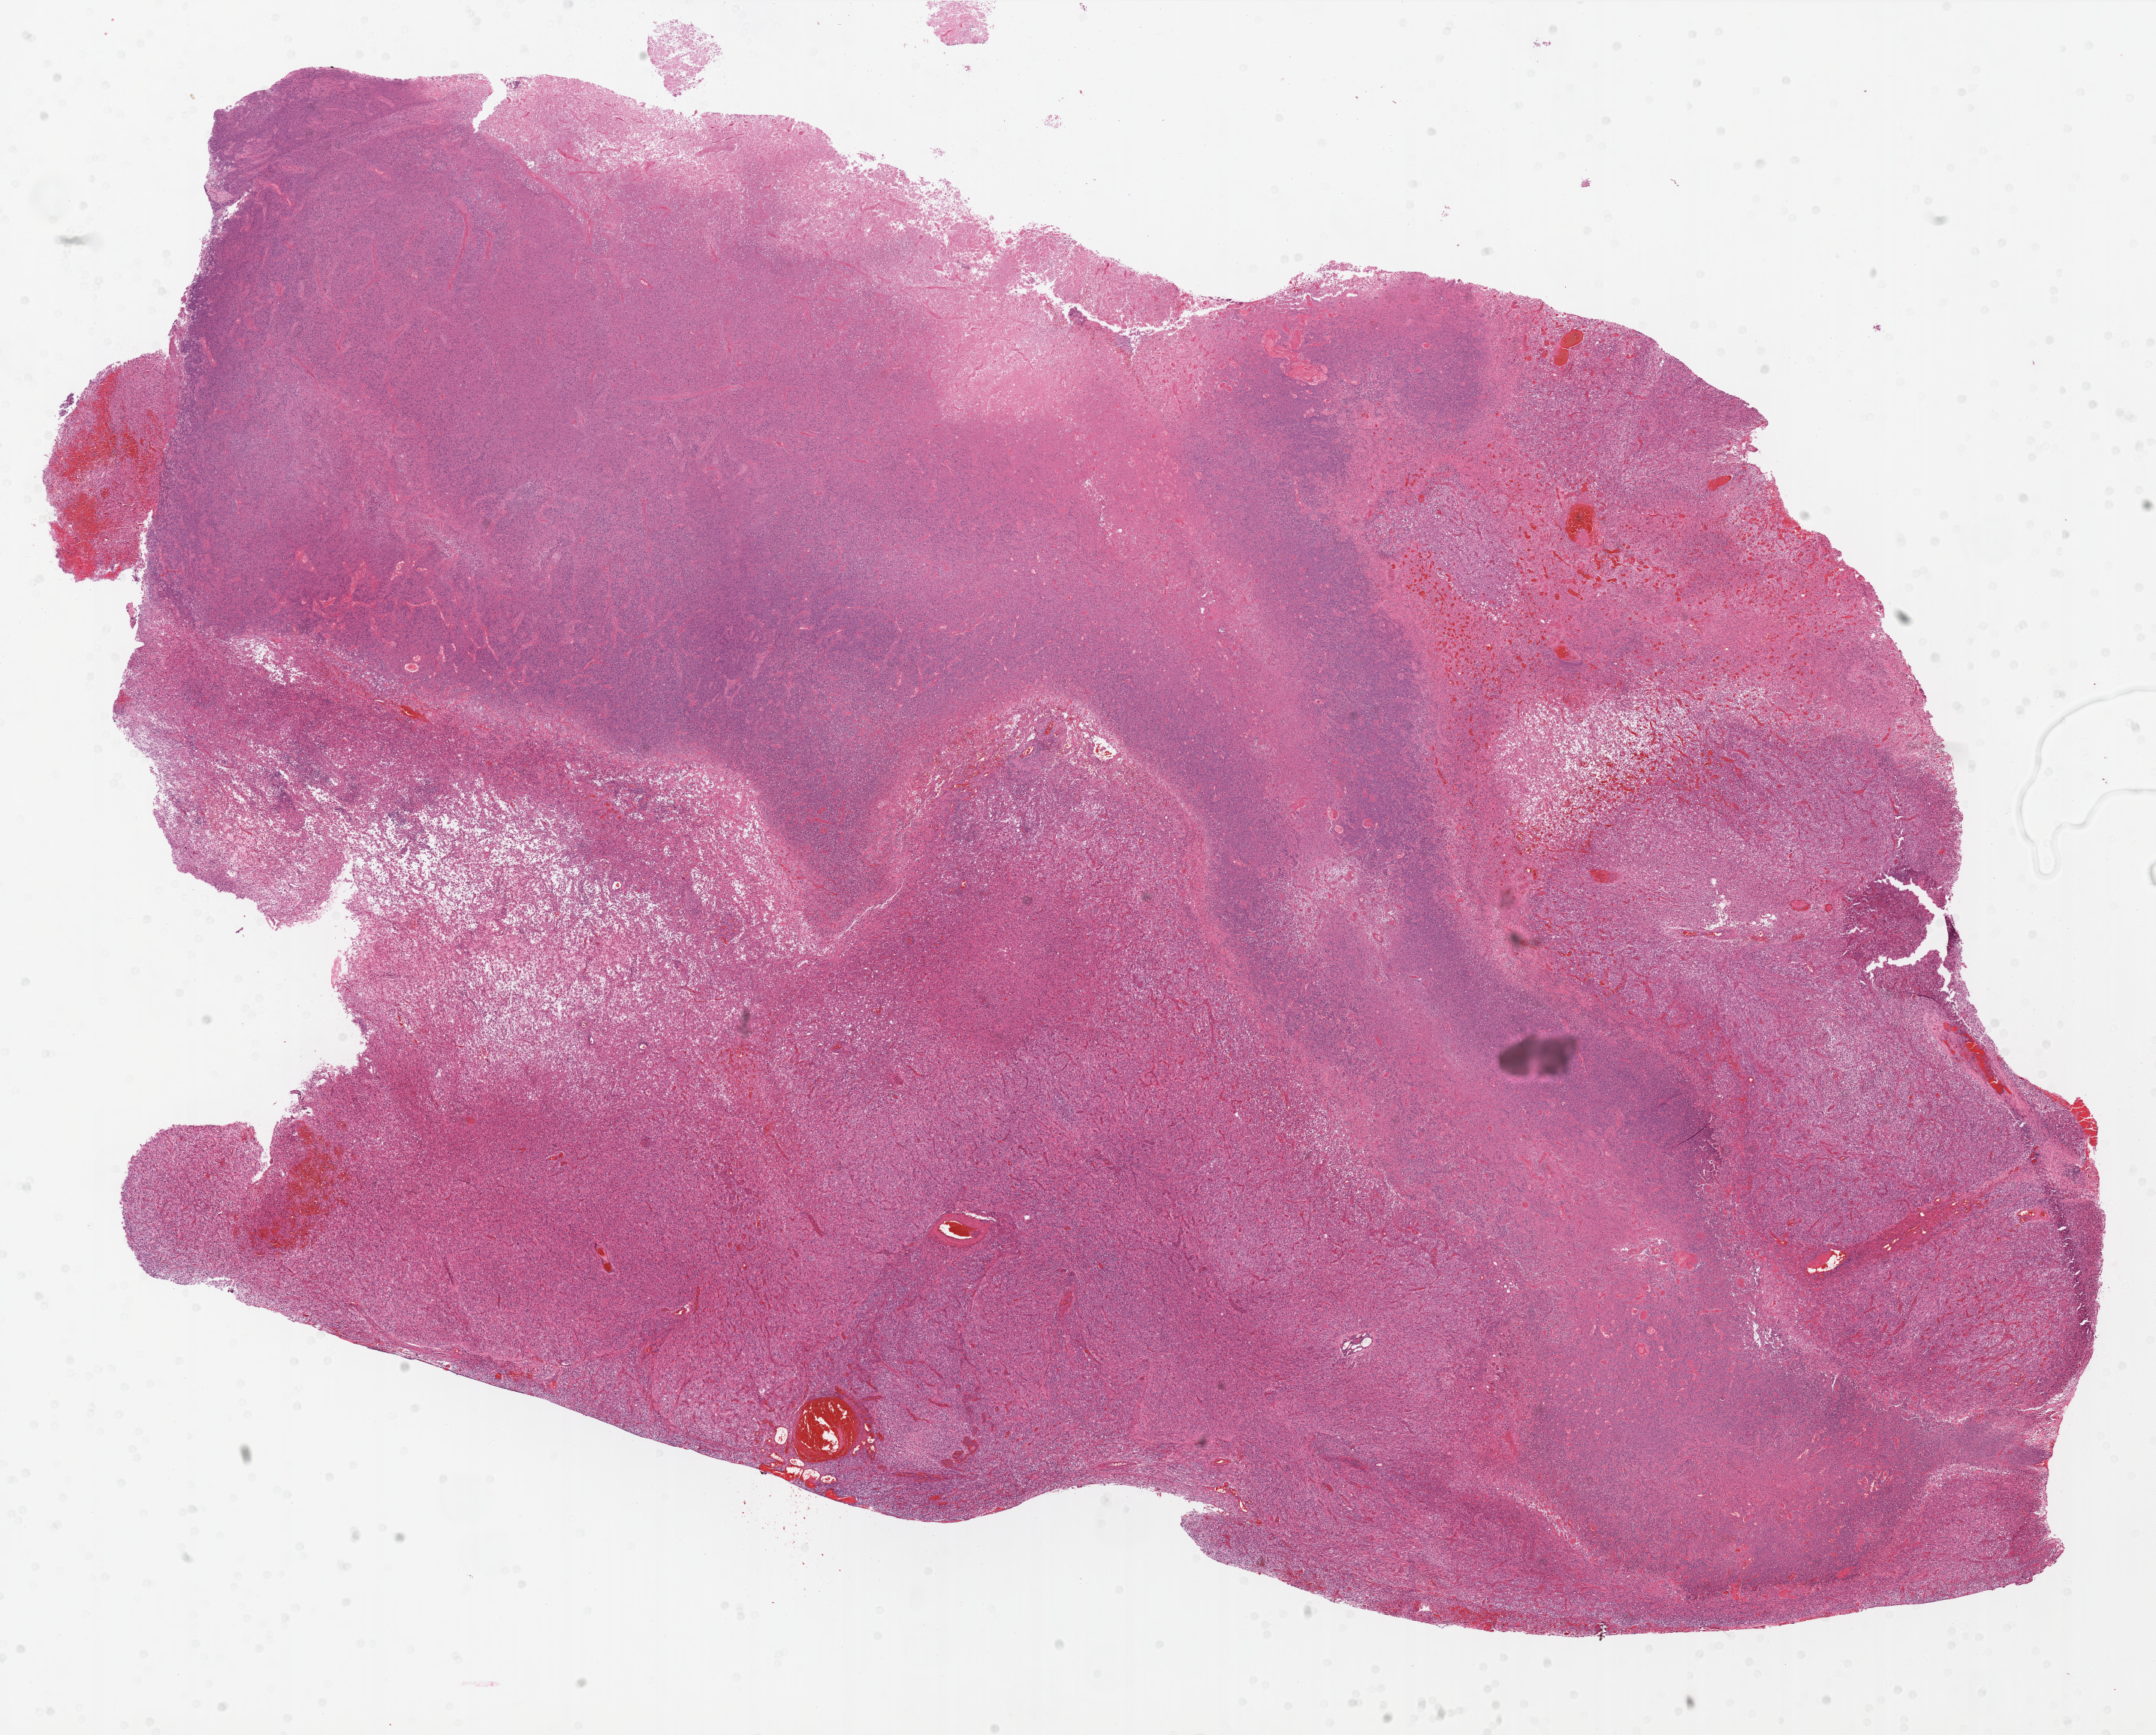
Whole-slide histology image, Hematoxylin and eosin (H&E) stained — whole scanned area (about 23.0 x 18.5 mm, acquisition: 20x scan) shown as a low-resolution overview, formalin-fixed paraffin-embedded (FFPE) diagnostic section, primary tumour sample from the brain. Female patient; age at initial diagnosis 52 years.
Pathologic diagnosis: Glioblastoma.